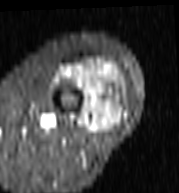
MRI of an extremity soft-tissue mass, one axial slice; slice 40 of 103 in the series (ordered by position); STIR; MR volume resampled by the dataset authors to the PET/CT grid (not the native acquisition matrix); 179 × 193 image matrix, field of view 175 × 188 mm. Female patient. Case-level facts recorded for this patient, not image findings: histological type: undifferentiated – high grade; grade: high; site of the primary tumour: left thigh.
Structures marked on this image (expert contour drawn on MRI and transferred to this co-registered scan by the dataset authors):
- gross tumour volume including surrounding oedema: box from (x=59, y=58) to (x=124, y=134) px
- gross tumour volume (mass): (x=88, y=66)–(x=122, y=134)